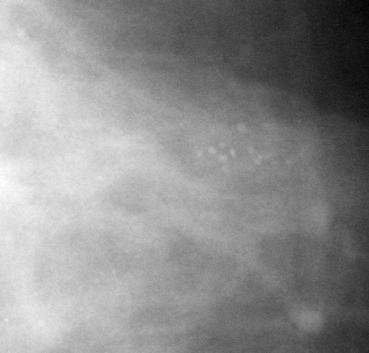
Cropped region of a digitized screen-film mammogram centred on a radiologist-marked abnormality; left breast; CC view; BI-RADS breast density category 3 (scale 1–4).
Calcifications, morphology punctate, distribution clustered; BI-RADS assessment category 4; subtlety rating 3 on a 1 (subtle) to 5 (obvious) scale; pathology result (as recorded, not read from the image): benign.